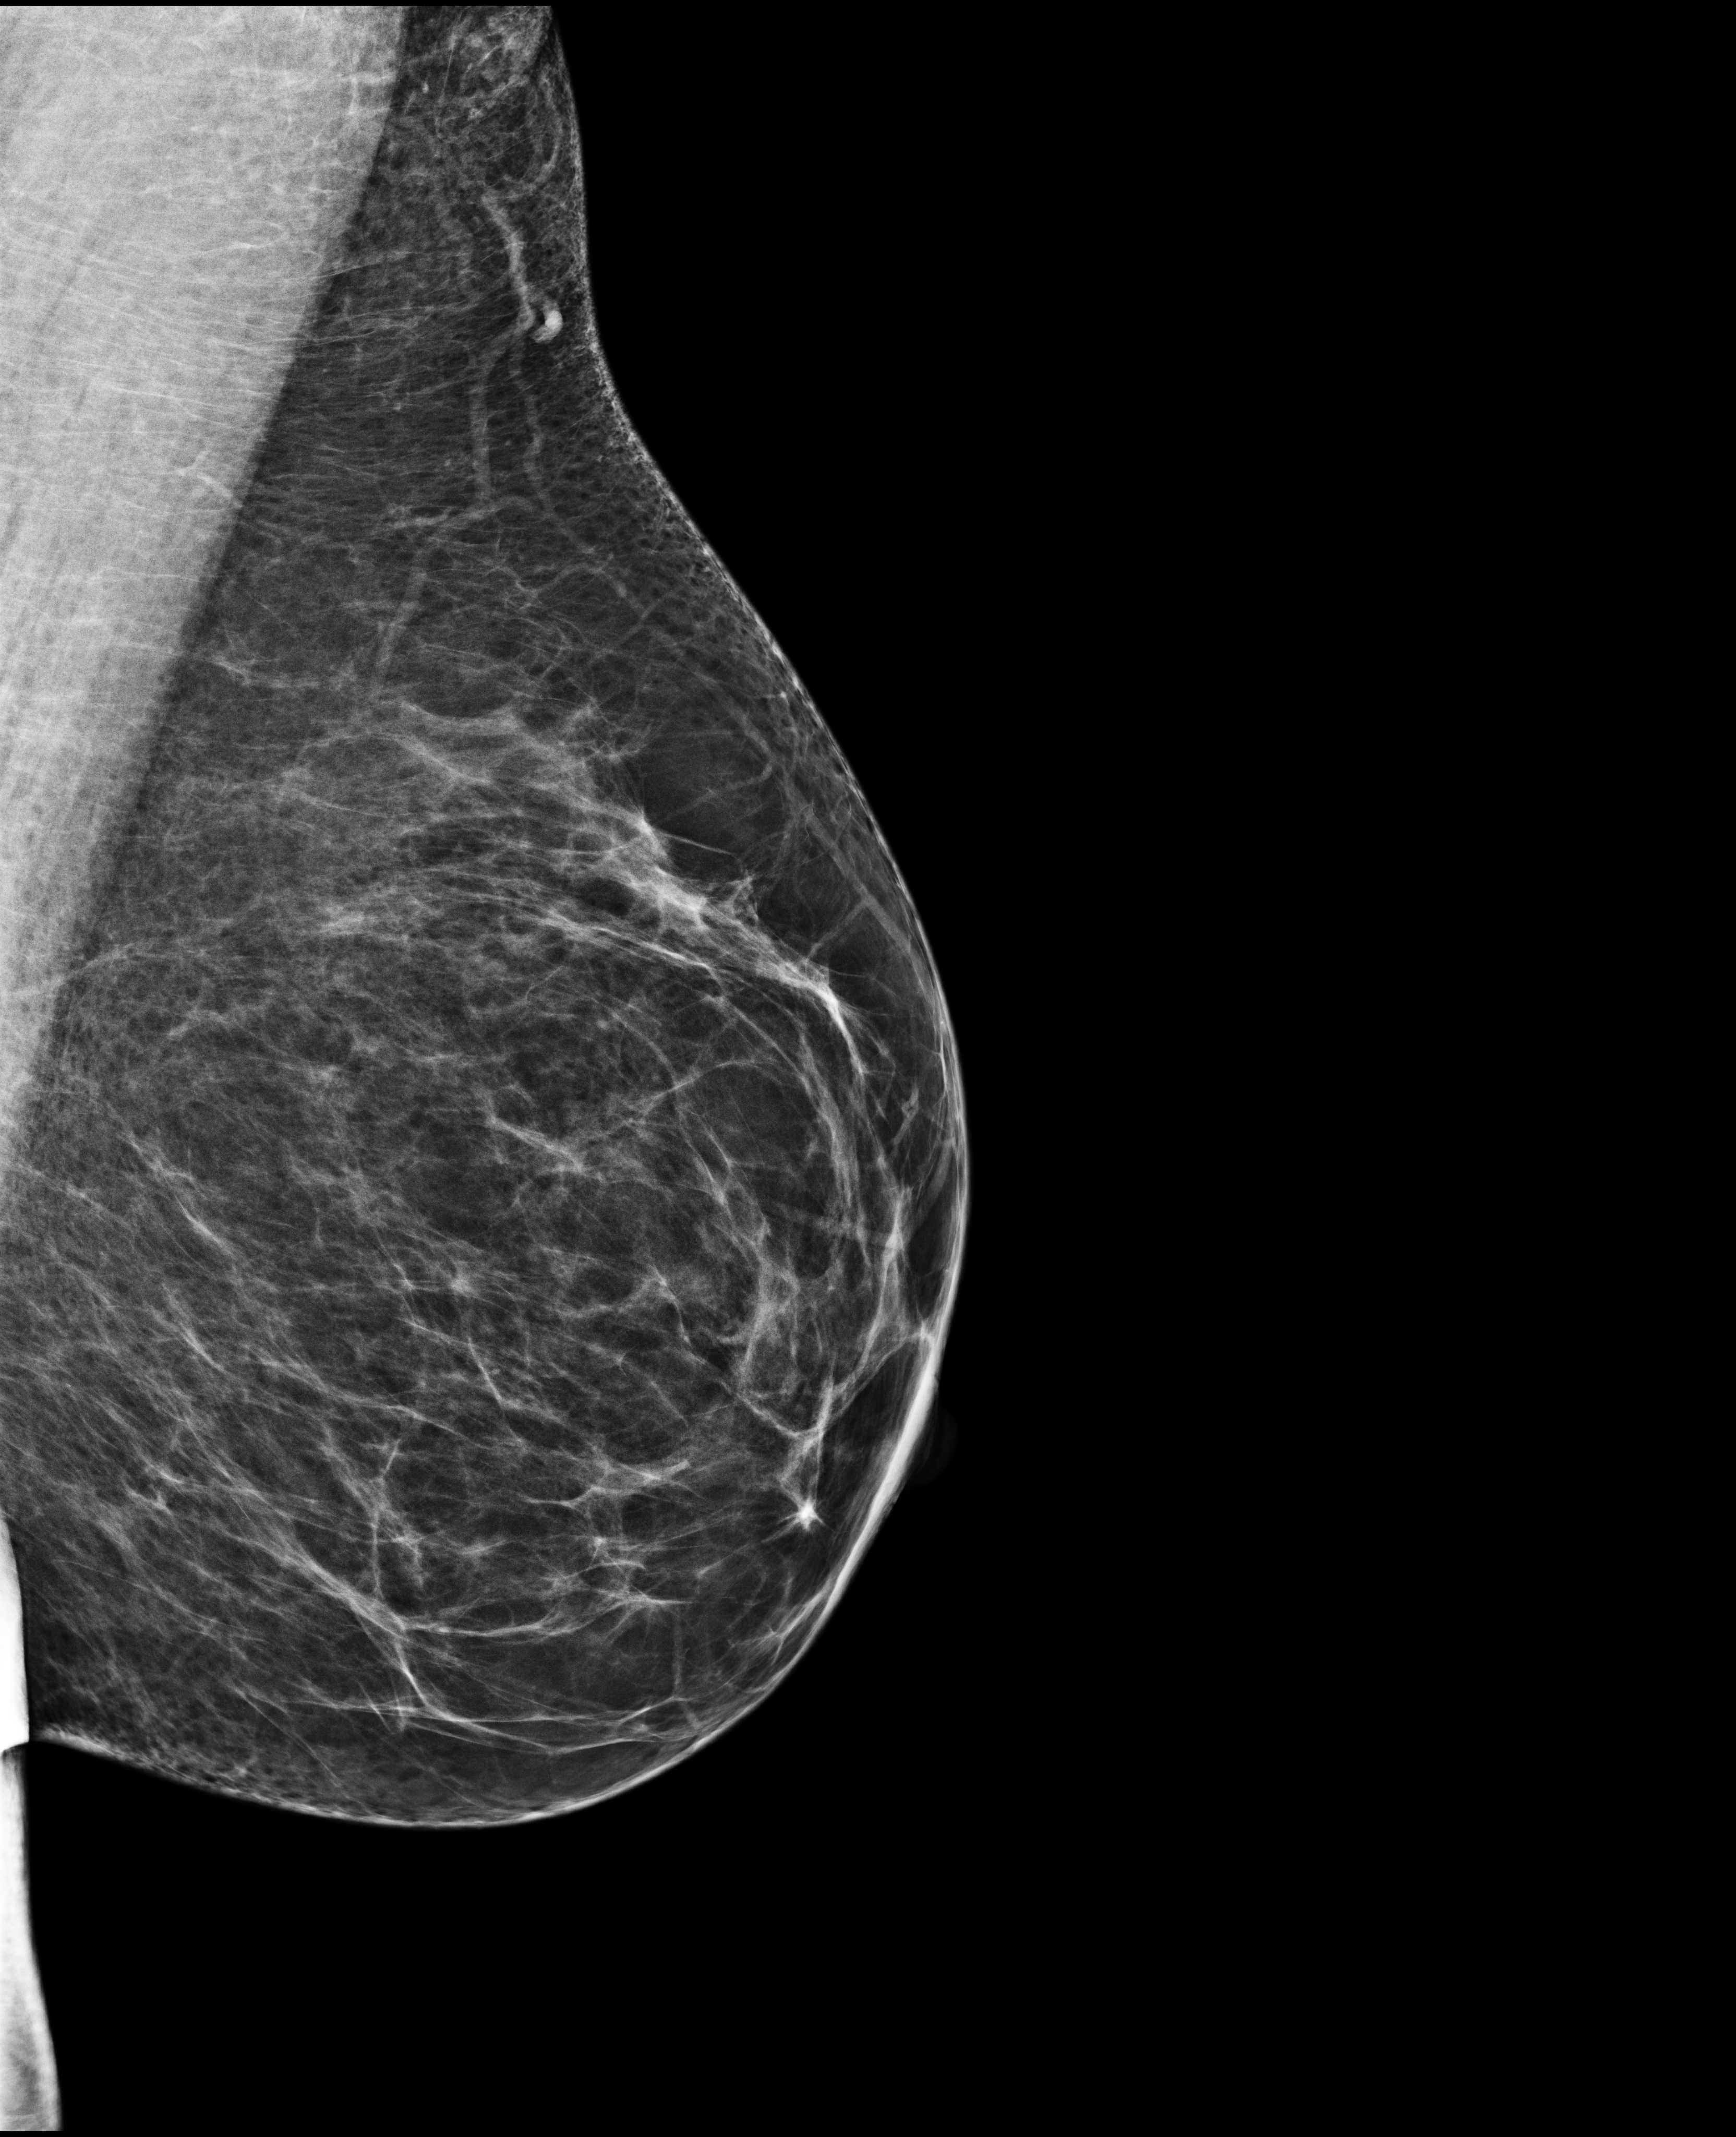
Screening examination. Patient: female, 42 years.
Image type: full-field digital mammogram. Breast: left. Projection: medio-lateral oblique projection.